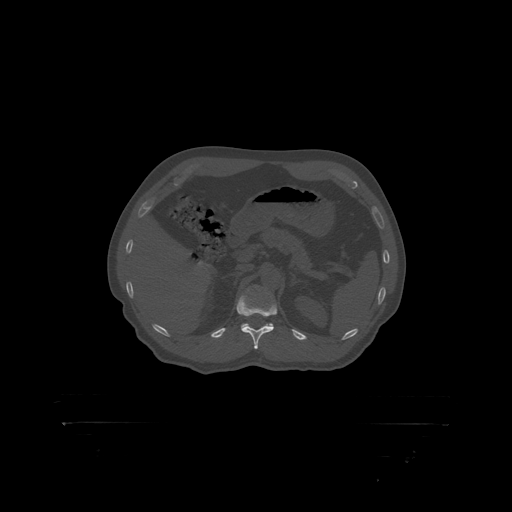
CT including the spine, one axial slice; reconstruction kernel STANDARD; 120 kVp; bone window (W 1800 / L 400 HU); 512 × 512 image matrix. Patient: male, 46 years. Case-level facts recorded for this patient, not image findings: primary cancer: skin.
Outlined on this slice (semi-automatically segmented with operator editing):
- T12 vertebra: bounding box <237,296,277,317> (left, top, right, bottom; pixels)